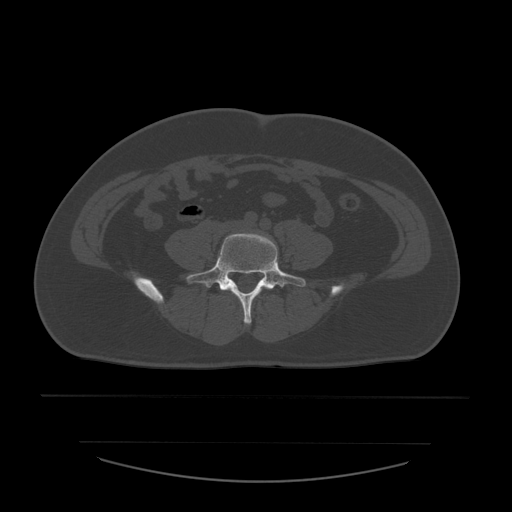
CT including the spine, one axial slice; position 125 of 532 along the scan axis; 120 kVp; bone window (W 1800 / L 400 HU); 512 × 512 image matrix, field of view 441 × 441 mm. Patient age 44 years. Case-level facts recorded for this patient, not image findings: primary cancer: soft tissue sarcoma.
Annotated regions visible in this slice (semi-automatically segmented with operator editing):
- L5 vertebra: box from (x=186, y=234) to (x=306, y=324) px